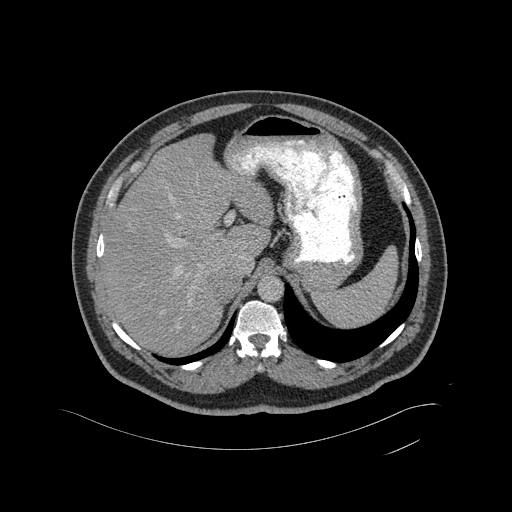
Contrast-enhanced abdominal CT, one axial slice. Position 344 of 433 along the scan axis. 120 kVp. Intravenous contrast given. Soft-tissue window (W 400 / L 40 HU). 2 mm slice thickness. 512 × 512 image matrix. Patient: male, 56 years. From the clinical record (not read from this slice): diagnosis: adrenocortical carcinoma; tumour side: right adrenal.
Annotated regions visible in this slice (semi-automatically segmented with operator editing):
- mass: box from (x=213, y=268) to (x=237, y=301) px